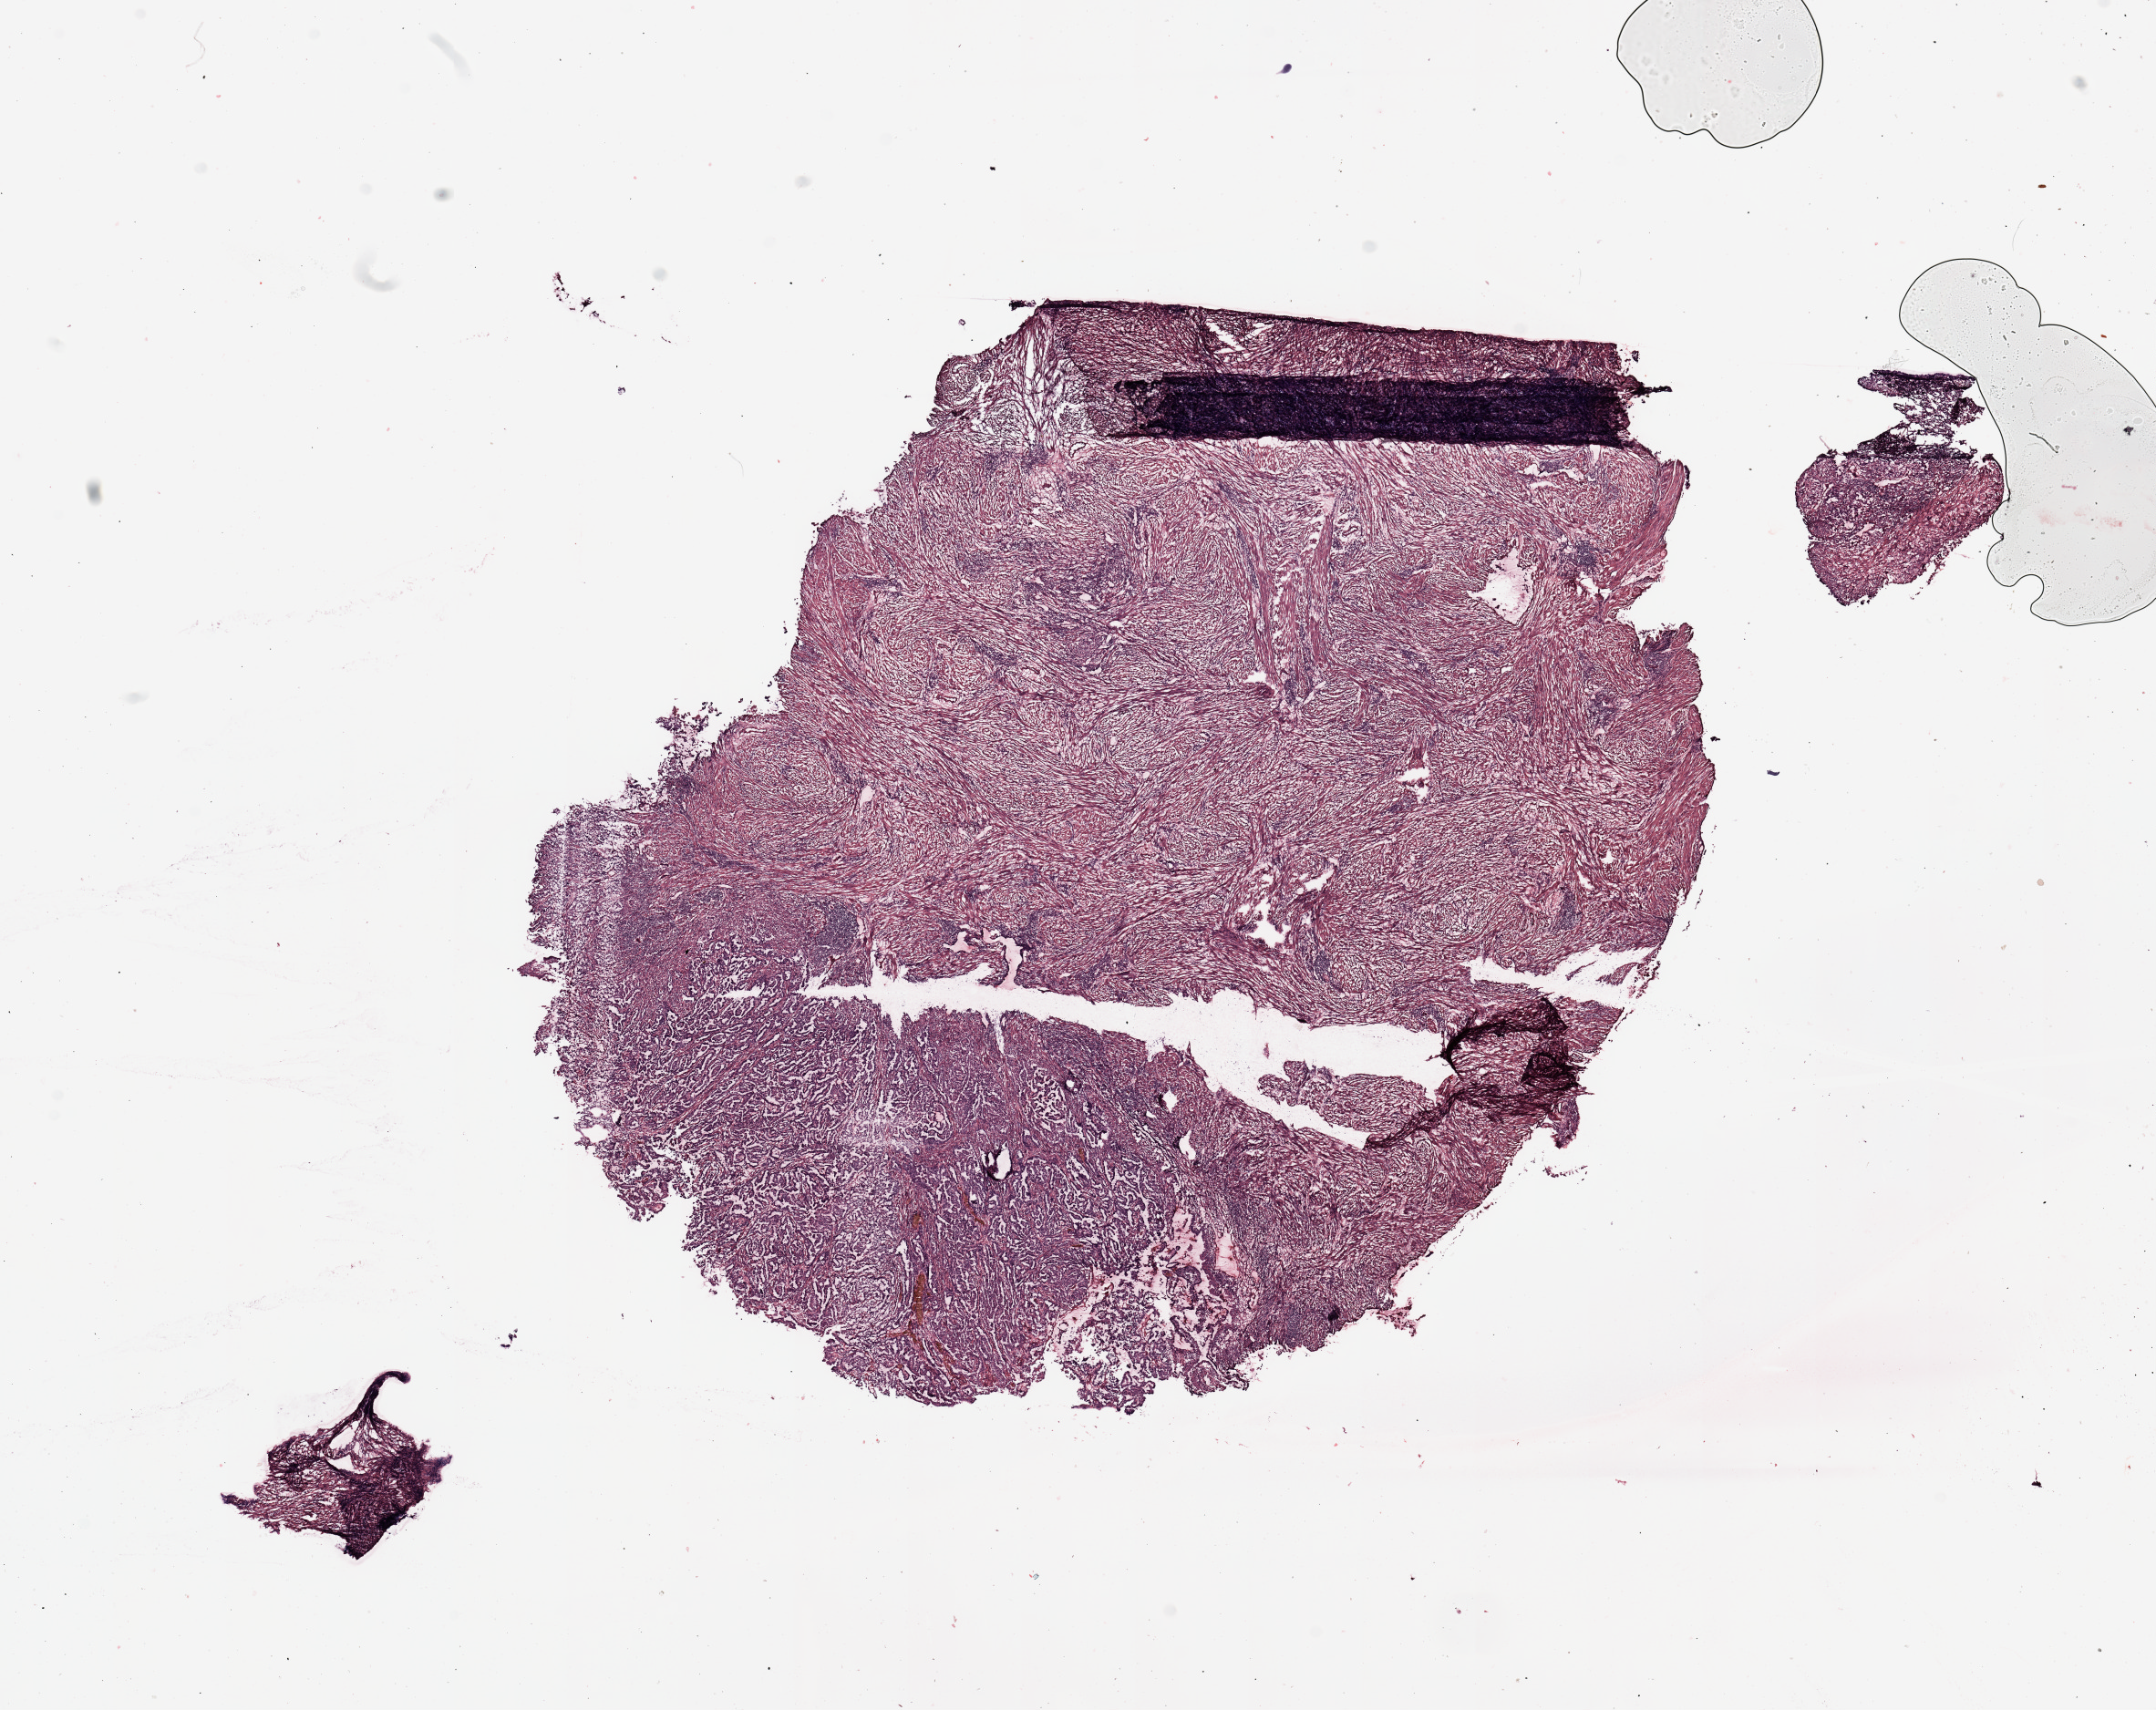
Digitized H&E tissue section (whole slide), low-resolution overview of the scanned area, about 18.7 x 14.8 mm, uterus, tumour tissue. 57-year-old female patient. Histologic grade: G3 (poorly differentiated).
AJCC pathologic stage: I. Diagnosis: Endometrioid adenocarcinoma, NOS.